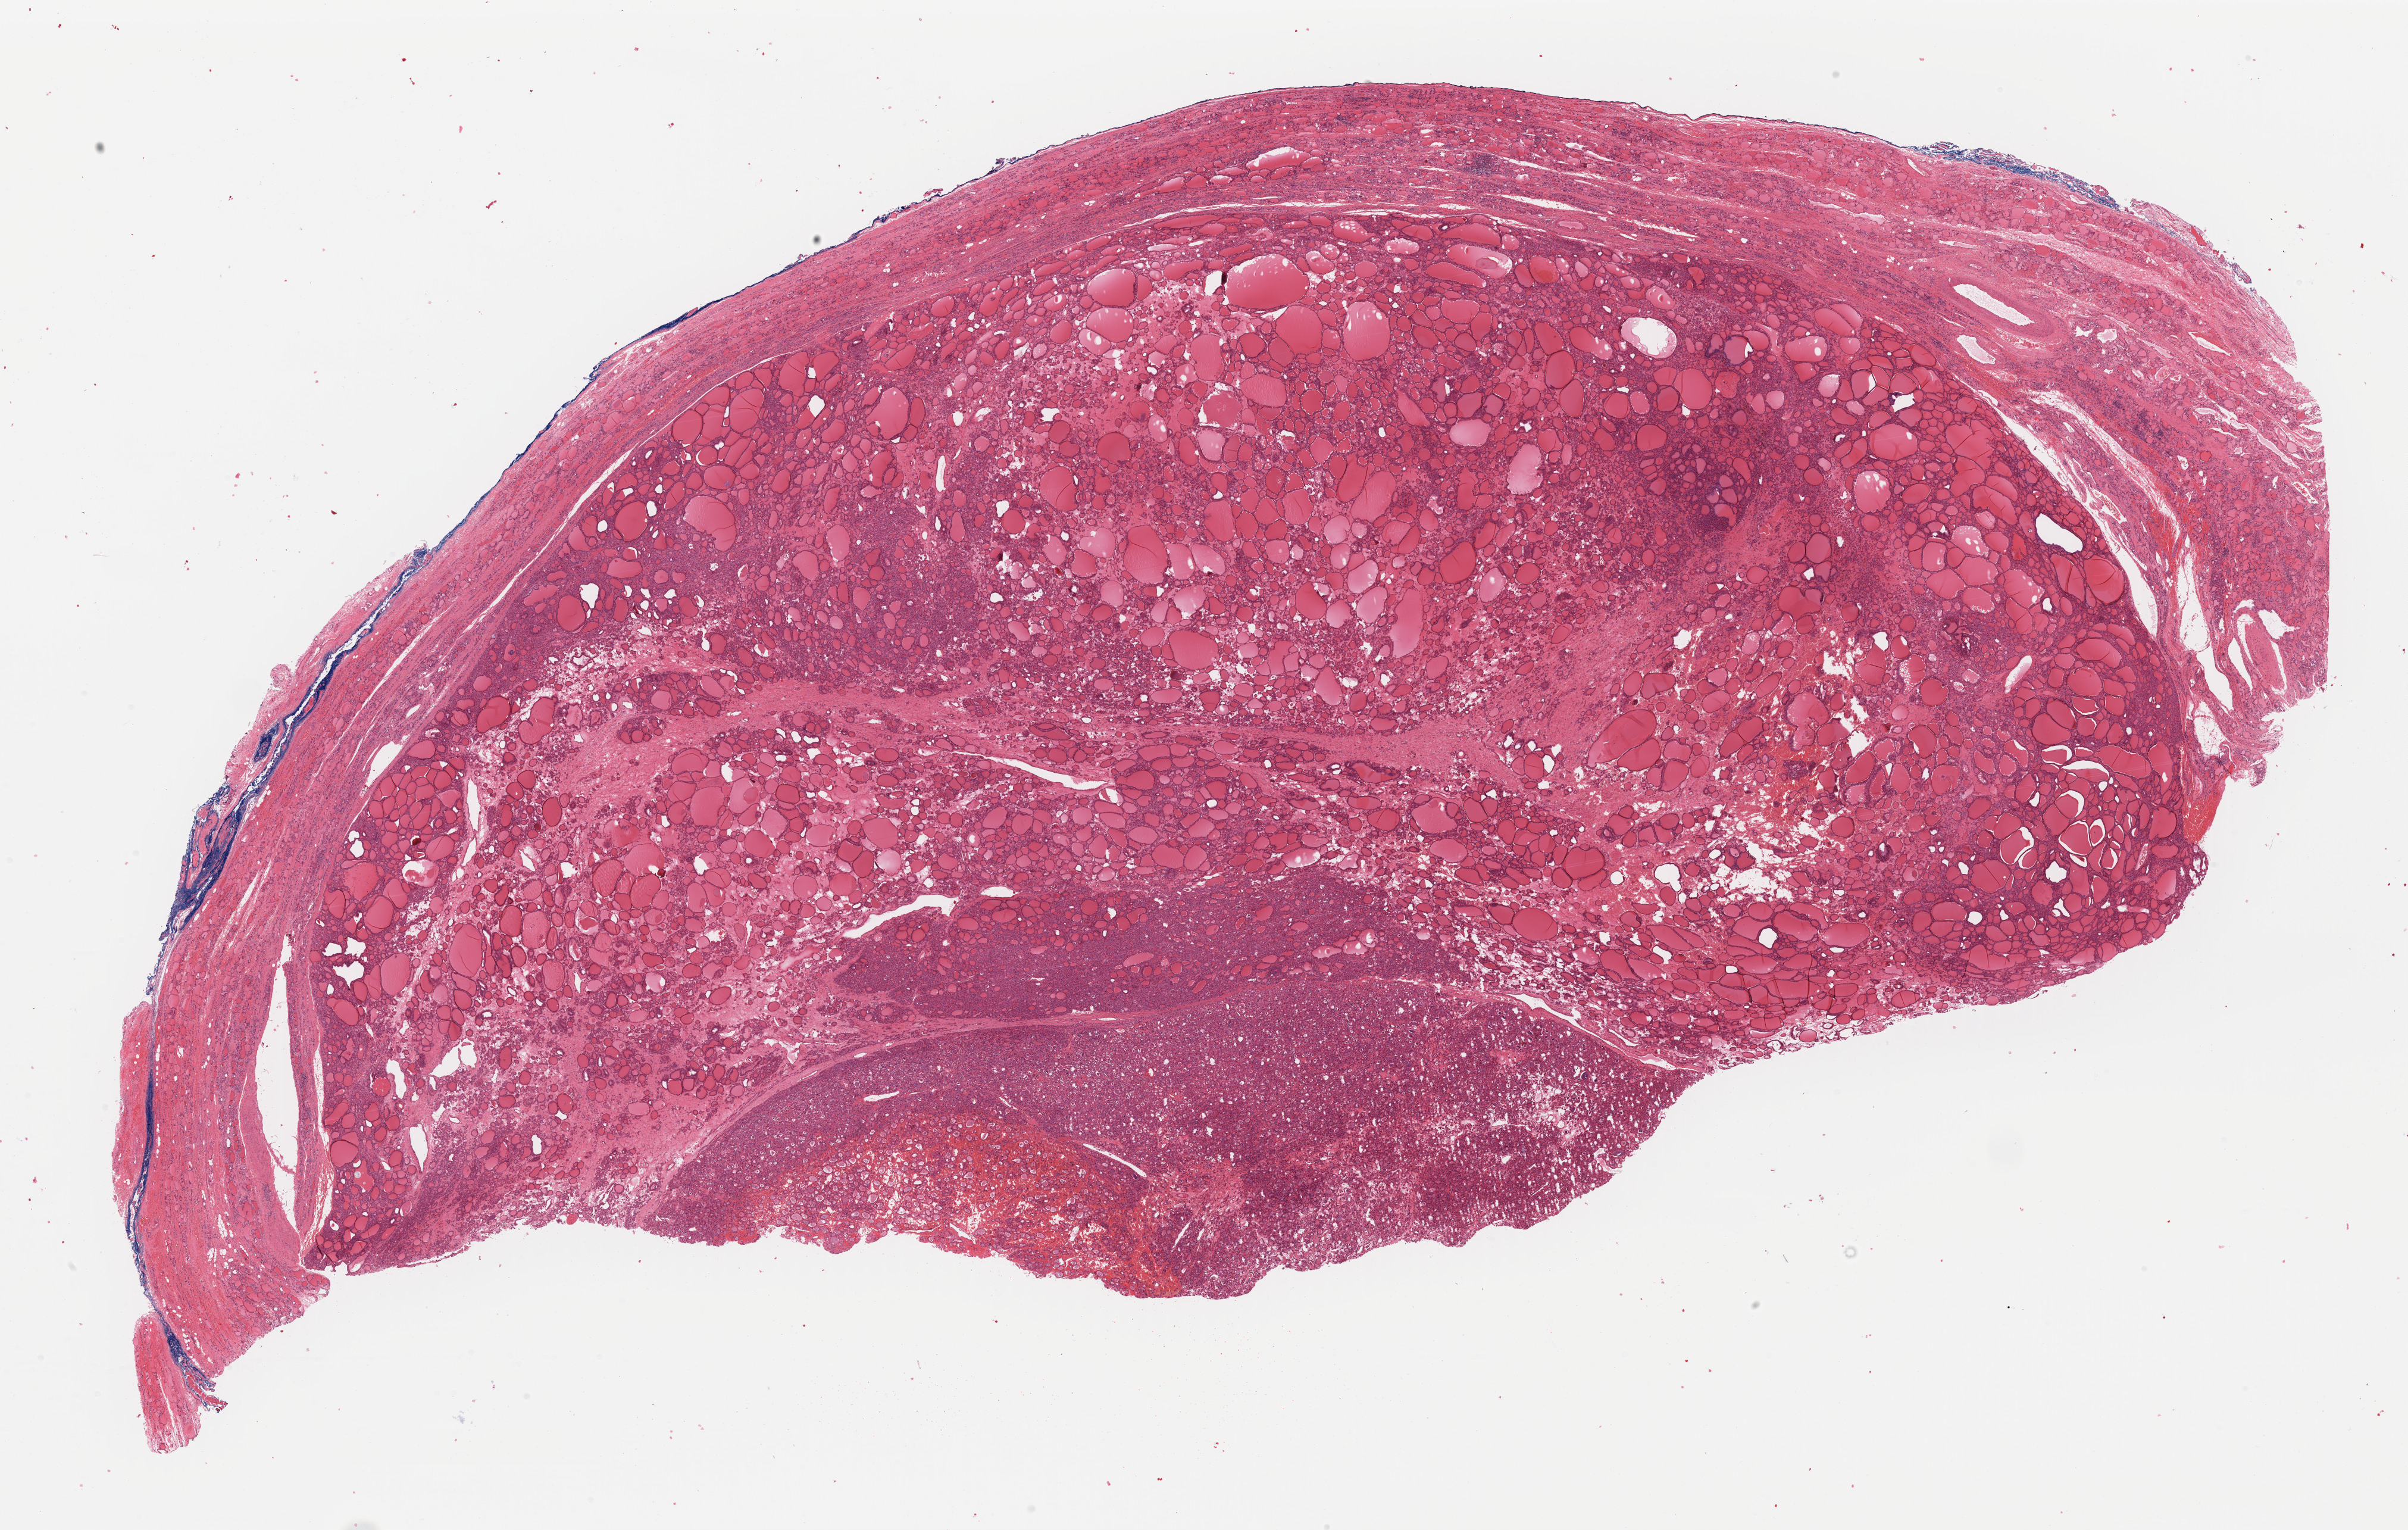
H&E whole-slide image — shown as a low-resolution overview of the whole scanned area (about 31.9 x 20.3 mm); formalin-fixed paraffin-embedded (FFPE) diagnostic section; sample: primary tumour, thyroid. Female patient; age at initial diagnosis 74 years.
- AJCC pathologic stage: II
- diagnosis: Papillary carcinoma, follicular variant (thyroid gland)
- TNM: T2 NX MX